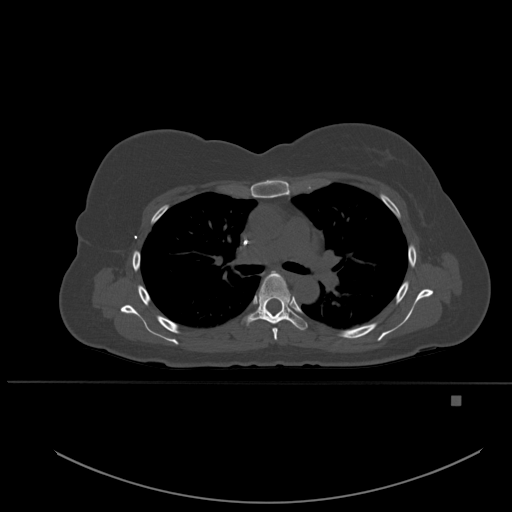
CT including the spine, one axial slice; slice 368 of 651 in the series (ordered by position); bone window (W 1800 / L 400 HU); 1.5 mm slice thickness; 512 × 512 image matrix, field of view 443 × 443 mm. Patient: female, 49 years. From the clinical record (not read from this slice): primary cancer: breast.
Outlined on this slice (semi-automatic segmentation, software-assisted and operator-edited):
- T4 vertebra: bounding box (x1, y1, x2, y2) in pixels: (262, 271, 278, 340)
- T5 vertebra: (244, 272, 308, 330)